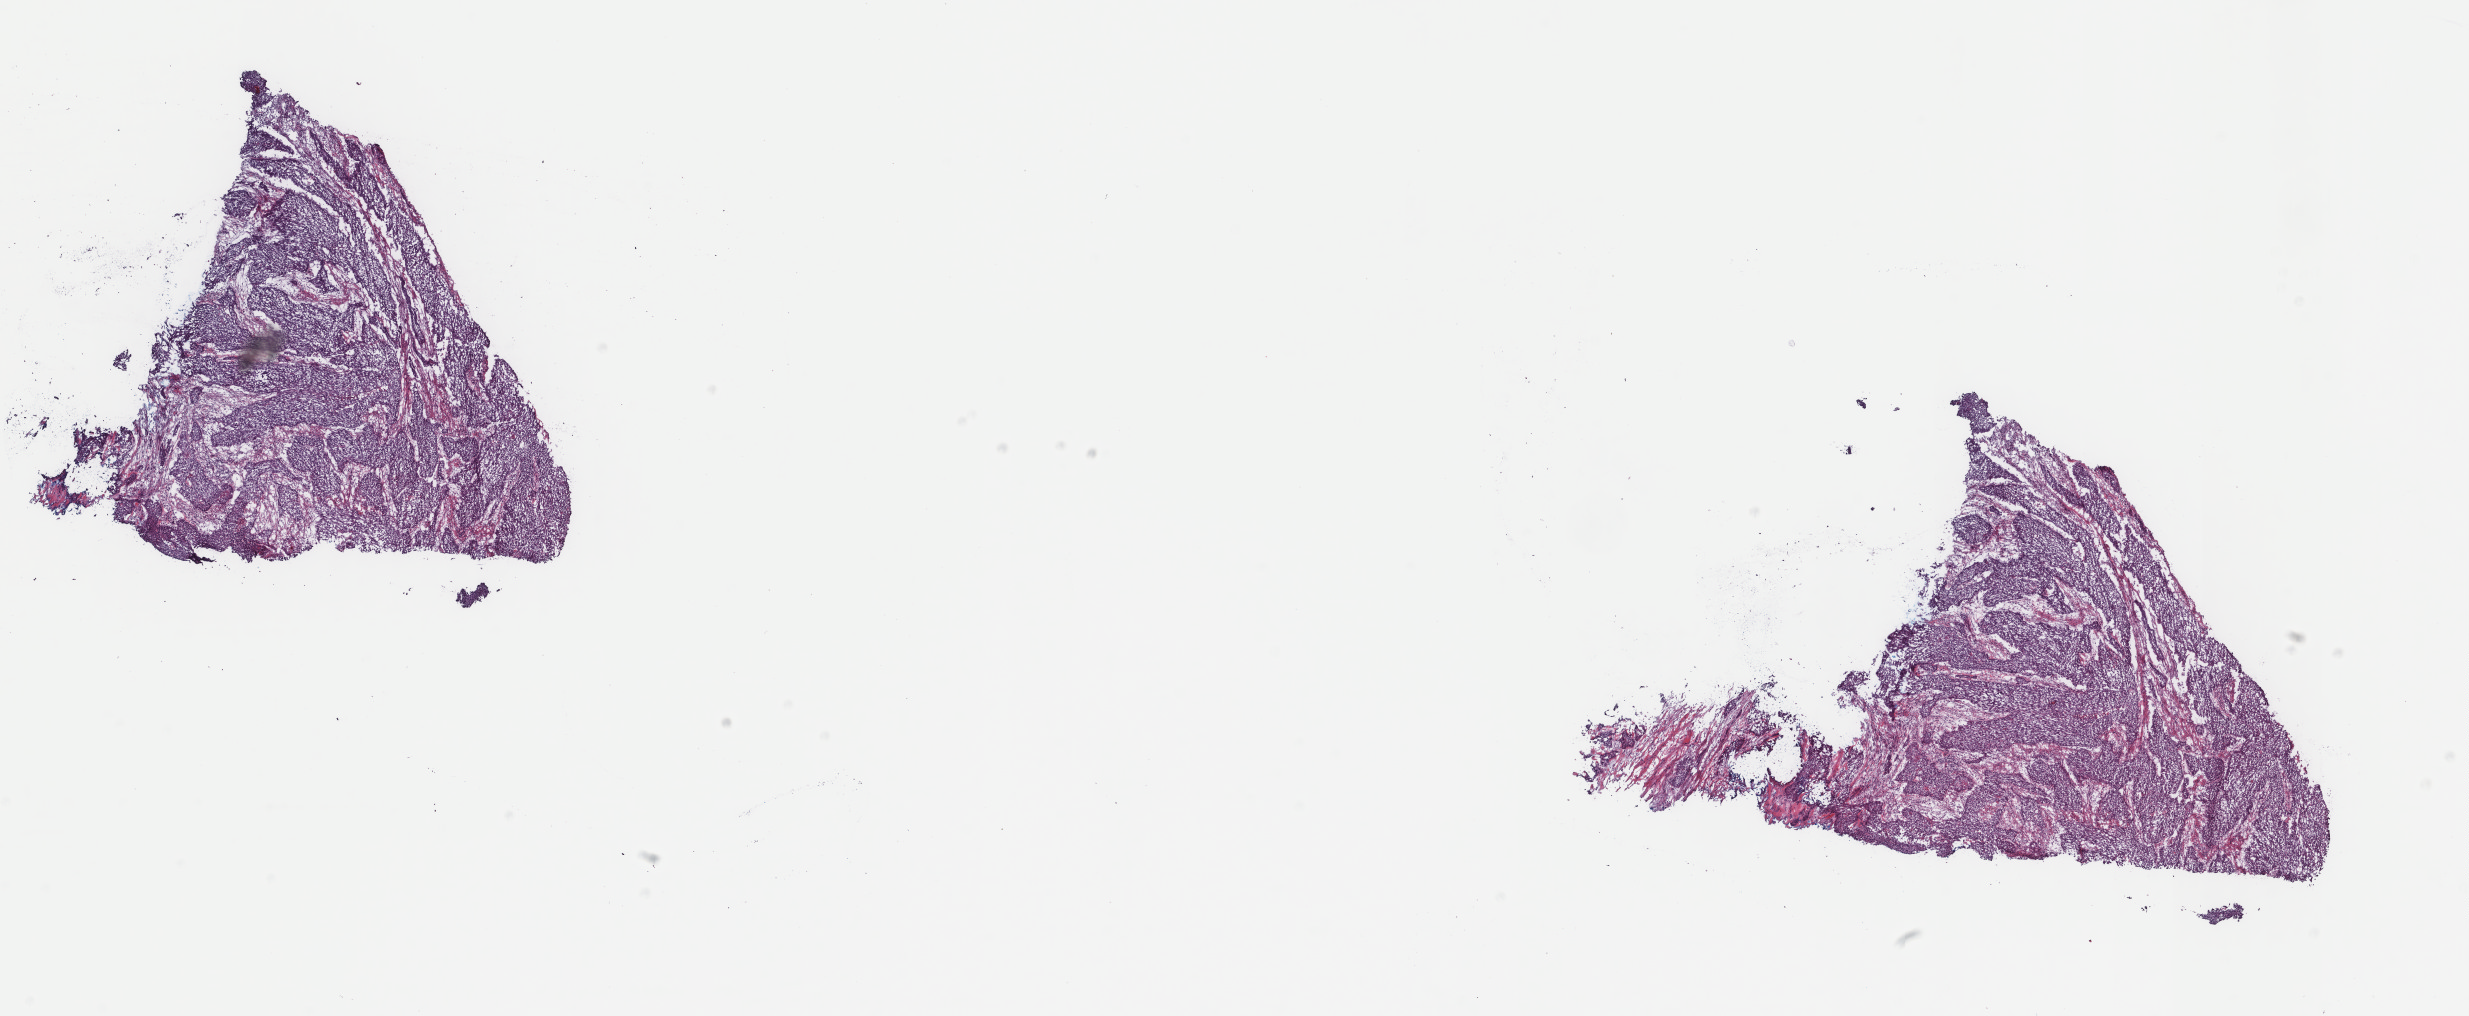
H&E-stained whole-slide image — whole scanned area (about 19.6 x 8.1 mm, from a 40x scan) shown as a low-resolution overview; frozen section from the top of the tissue portion; primary tumour sample from the bladder. Male patient; age at initial diagnosis 45 years. Histologic grade: high grade. Slide review estimates, as recorded: tumour cells 80%, tumour nuclei 80%, normal cells 0%, stromal cells 20%, necrosis 0%. Inflammatory infiltration, as recorded: lymphocyte infiltration 2%, monocyte infiltration 1%, neutrophil infiltration 1%.
AJCC pathologic stage: III (7th edition). Pathologic diagnosis: Transitional cell carcinoma. TNM: T3a N0 M0. Lymph nodes positive (case pathology): 0 of 11 examined.